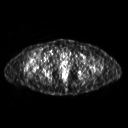
FDG PET of an extremity soft-tissue mass (from a PET/CT study), one axial slice; slice 285 of 311 in the series (ordered by position); 3.27 mm slice thickness; 128 × 128 image matrix, field of view 500 × 500 mm. Patient: female, 57 years. Case-level facts recorded for this patient, not image findings: histological type: pleiomorphic undifferentiated sarcoma; grade: high; site of the primary tumour: right quadricep.
Annotated regions visible in this slice (expert contour drawn on MRI and transferred to this co-registered scan by the dataset authors):
- tumour plus oedema (research contour): box from (x=26, y=57) to (x=39, y=67) px